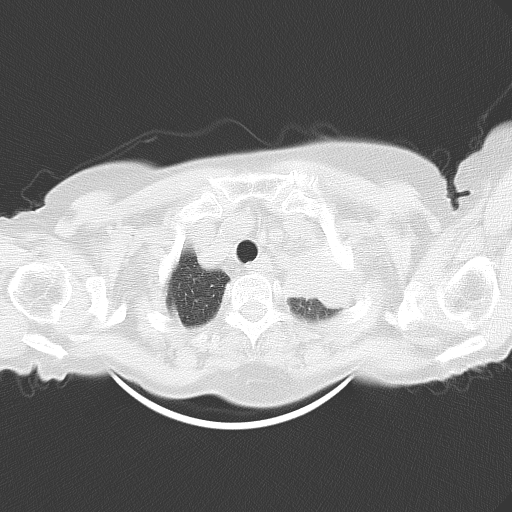
Chest CT, one axial slice; position 48 of 54 along the scan axis; reconstruction kernel B70f; 120 kVp; lung window (W 1500 / L -600 HU); 512 × 512 image matrix, field of view 353 × 353 mm. Patient: female, 71 years. Case-level facts recorded for this patient, not image findings: clinical TNM (as recorded): T3 N3 M0.
Annotated regions visible in this slice (bounding box drawn by a radiologist):
- lung tumour (recorded histology: adenocarcinoma): bounding box (x1, y1, x2, y2) in pixels: (269, 237, 372, 329)